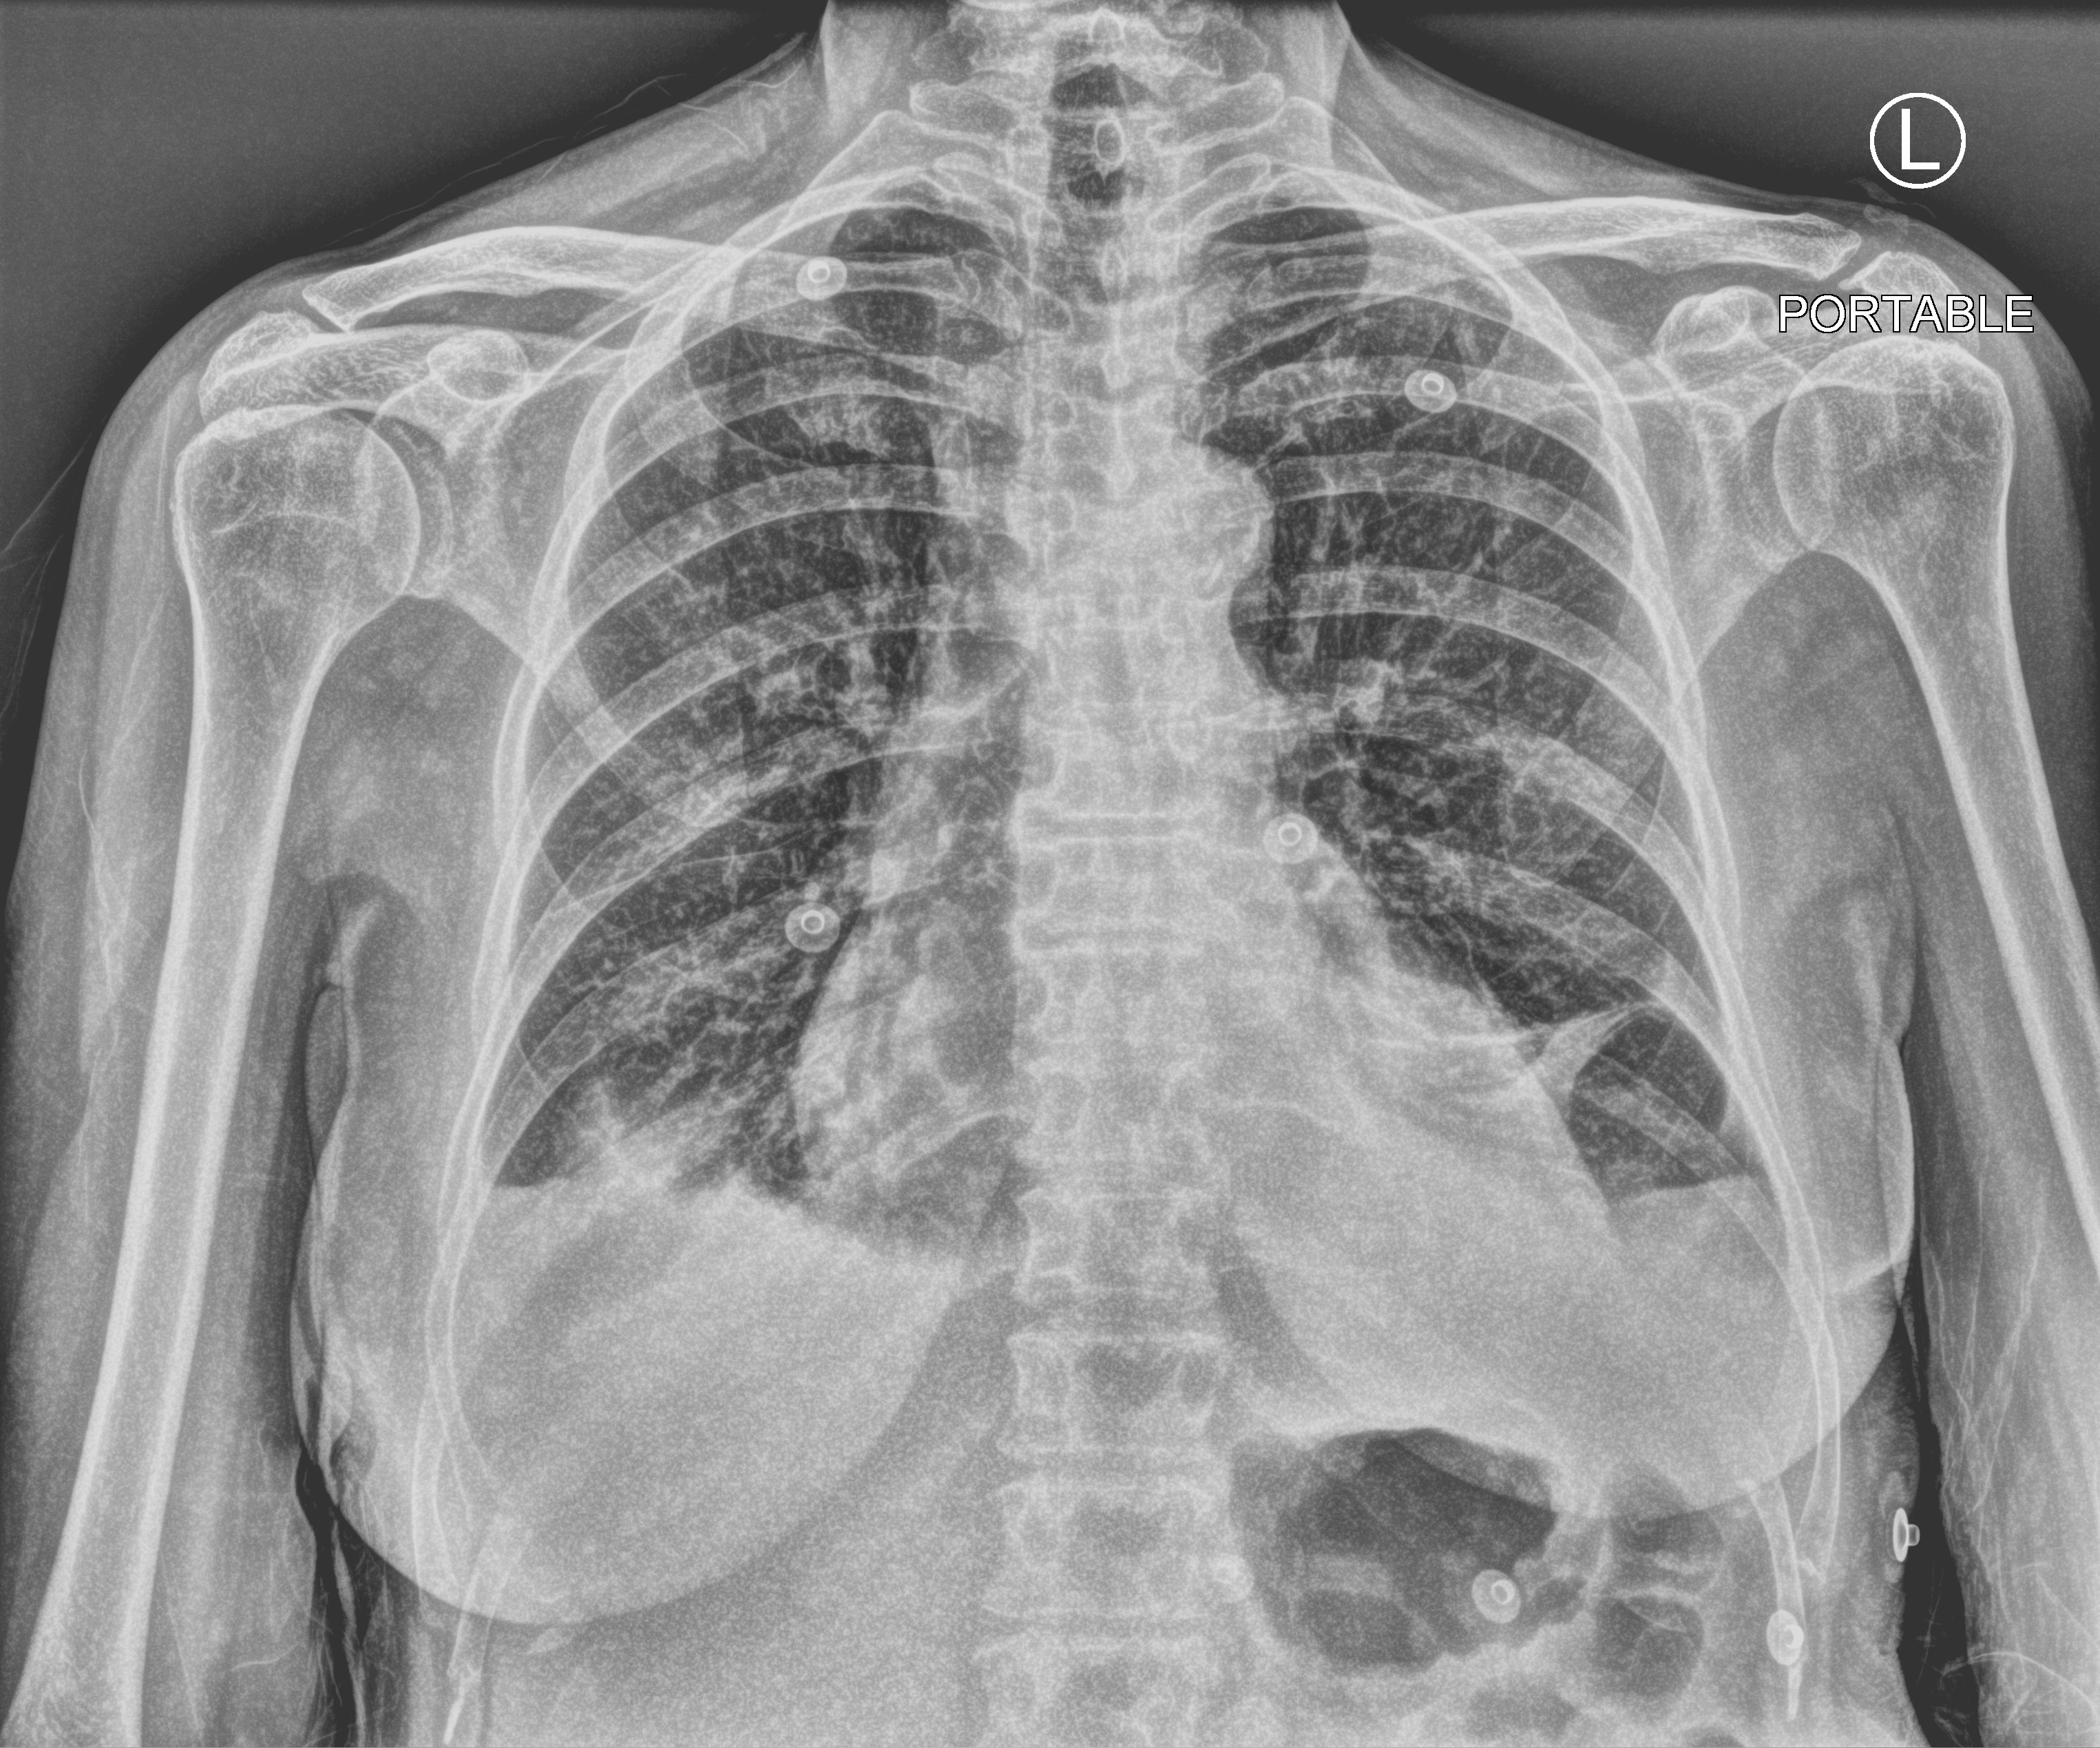
Chest X-ray (portable). Female patient hospitalised with COVID-19, age 75–90 years.
Admission-level facts for this patient (not findings on this image; timing relative to this image not recorded):
- admitted to intensive care during this hospital stay: no
- length of hospital stay: 3 days
- mechanically ventilated during this hospital stay: no